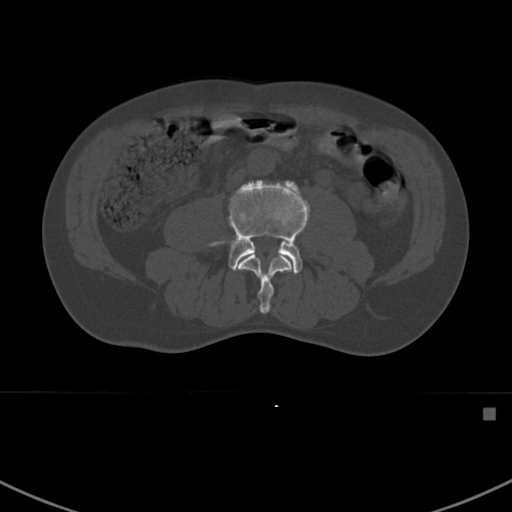
CT including the spine, one axial slice; position 251 of 412 along the scan axis; reconstruction kernel Br40s; bone window (W 1800 / L 400 HU); 1.5 mm slice thickness; 512 × 512 image matrix. Male patient, age 59 years. Case-level facts recorded for this patient, not image findings: primary cancer: prostate.
Outlined on this slice (semi-automatic segmentation, software-assisted and operator-edited):
- L3 vertebra: box from (x=236, y=252) to (x=295, y=313) px
- L4 vertebra: (x=209, y=178)–(x=310, y=274)